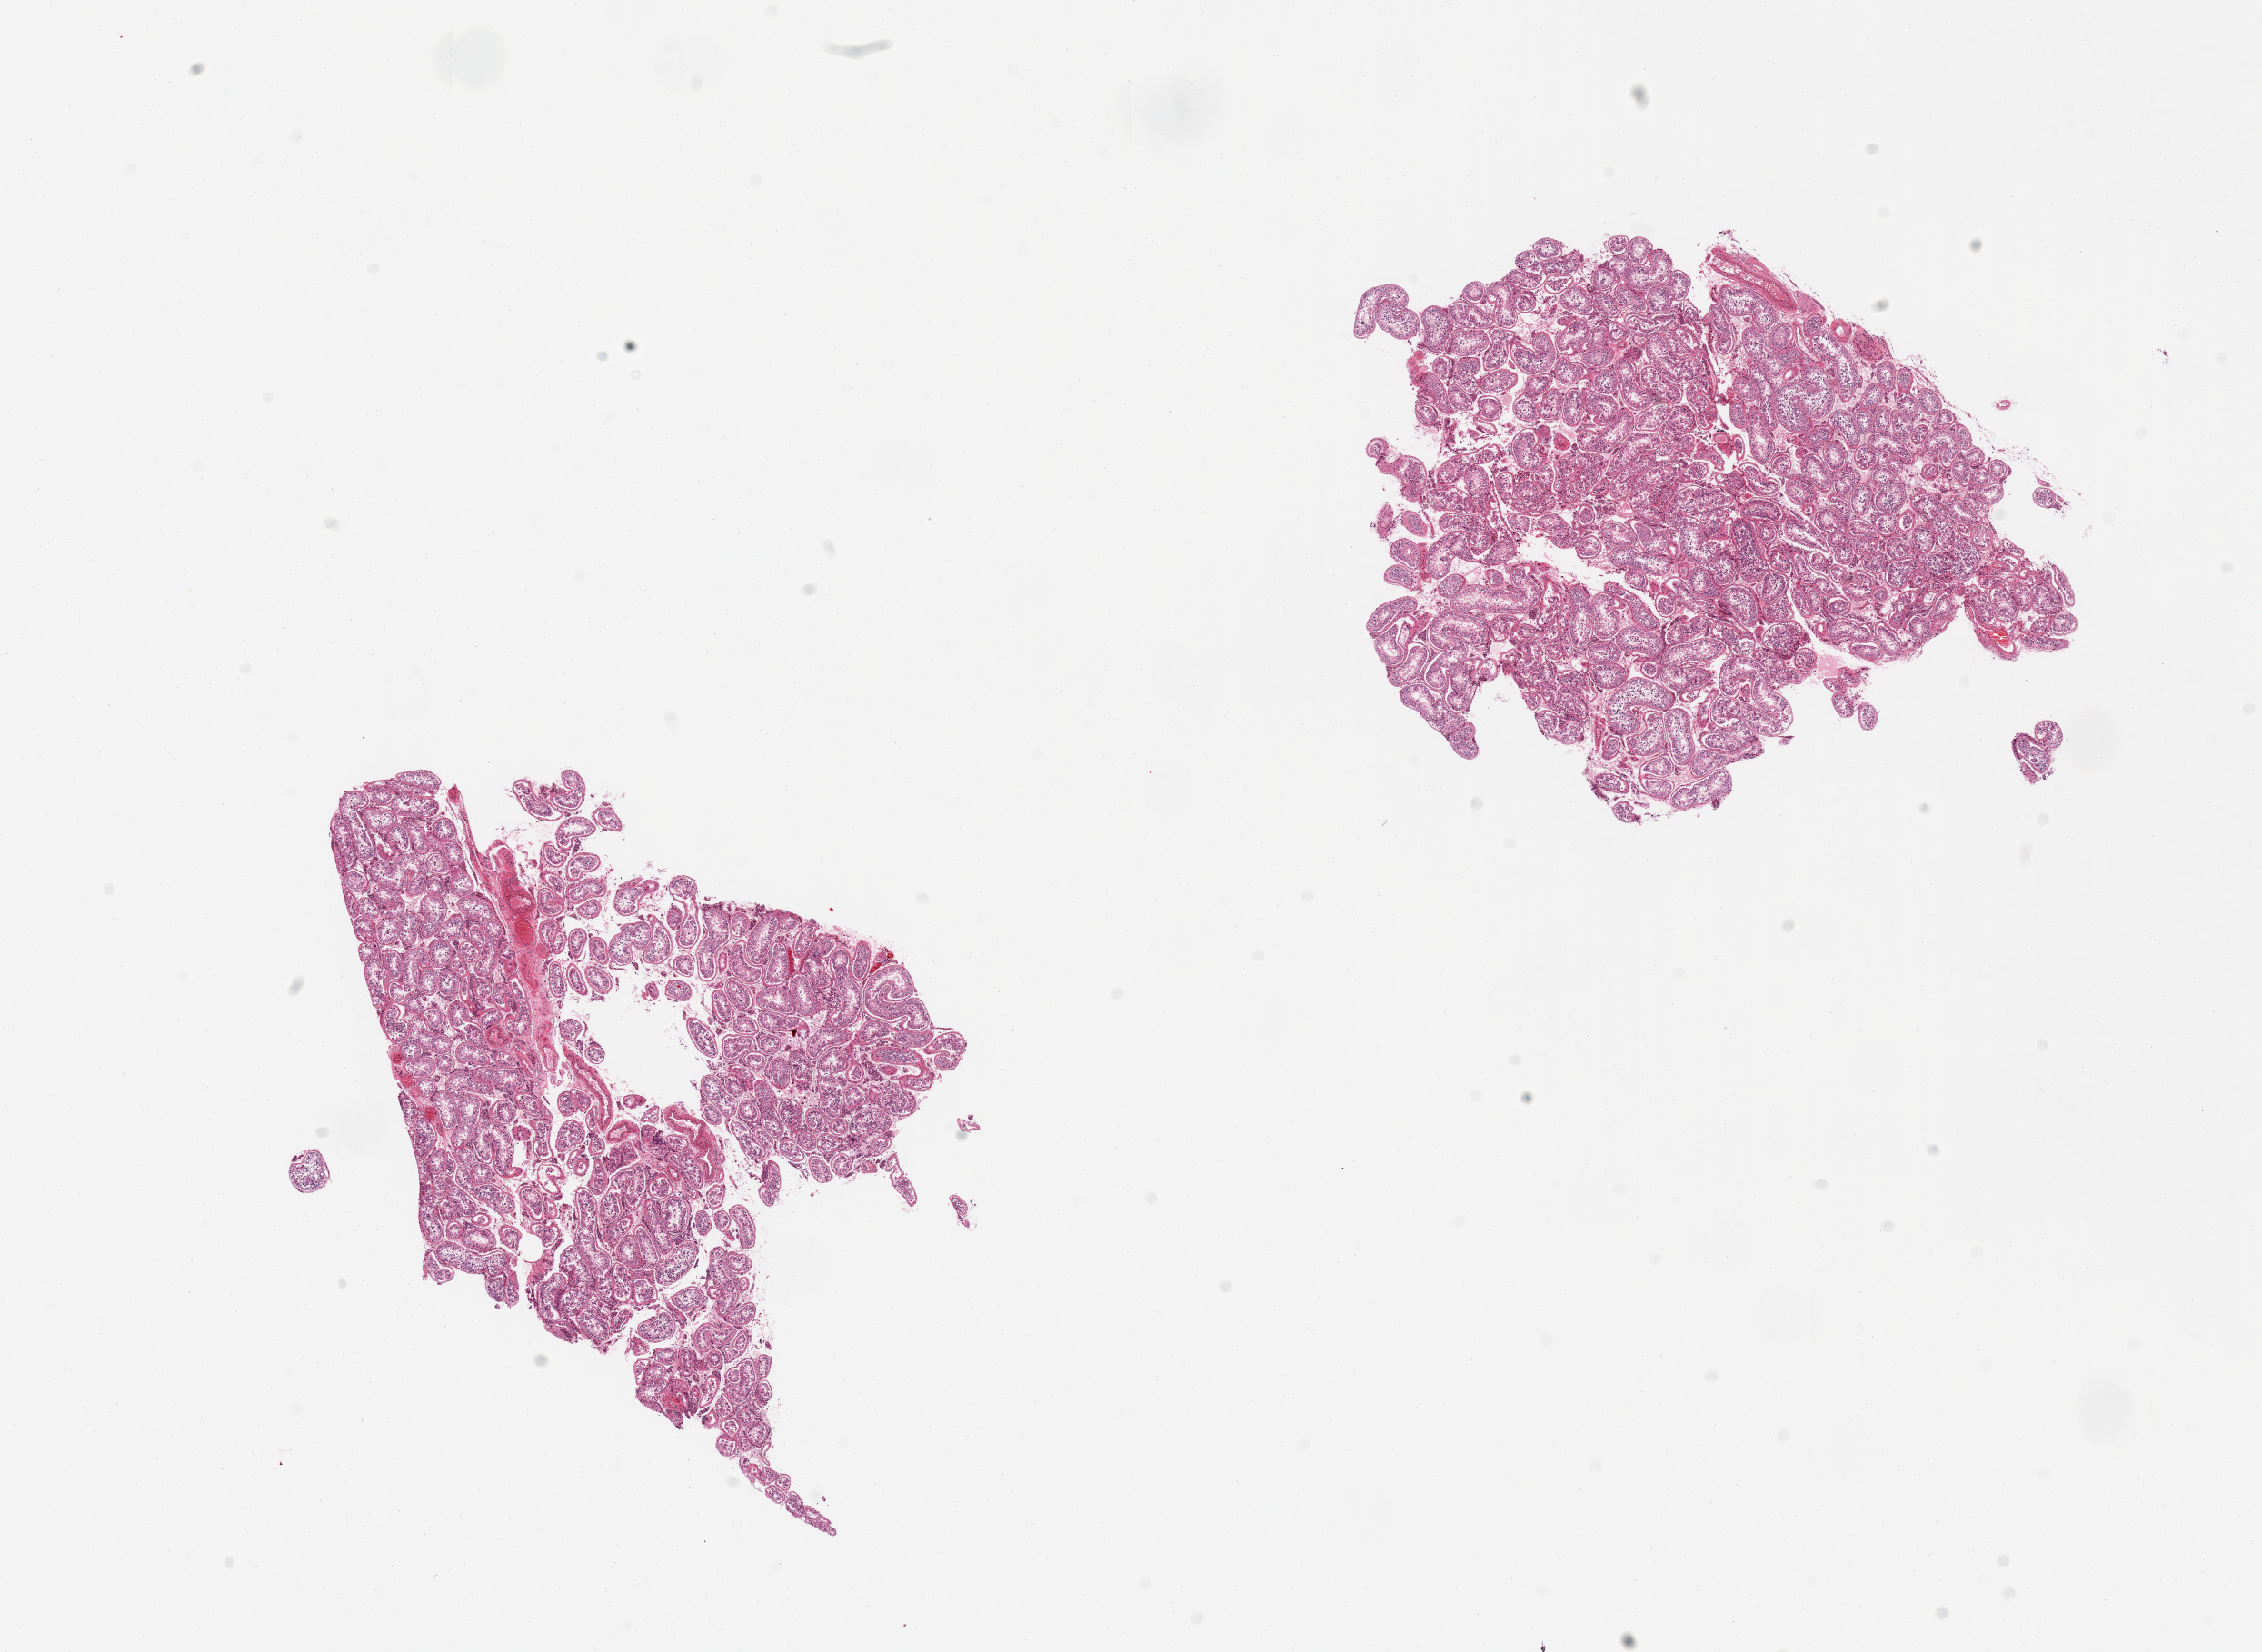
Whole-slide image, haematoxylin and eosin stain — low-resolution overview of the scanned area, about 19.7 x 14.4 mm (slide scanned at 20x). PAXgene-fixed, paraffin-embedded tissue. Target tissue: testis. Donor tissue sample. Donor: male.
Review note (as recorded): 2 pieces, decreased spermatogenesis and some Sertoli cell-only tubules.